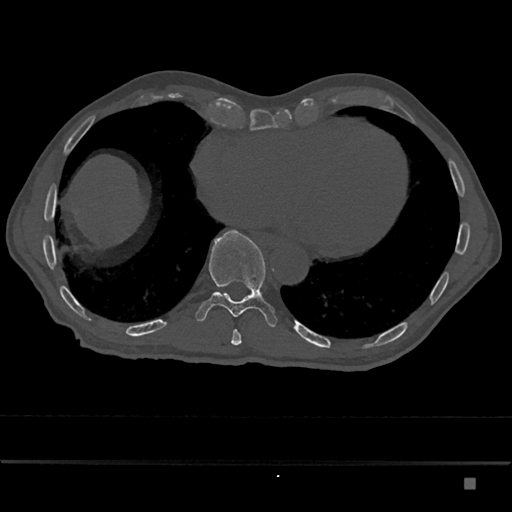
CT including the spine, one axial slice; position 746 of 797 along the scan axis; reconstruction kernel Br40s/3; bone window (W 1800 / L 400 HU); 0.5 mm slice thickness; 512 × 512 image matrix, field of view 390 × 390 mm. Male patient, age 72 years. From the clinical record (not read from this slice): primary cancer: prostate.
Outlined on this slice (semi-automatic segmentation, software-assisted and operator-edited):
- T10 vertebra: box from (x=196, y=230) to (x=277, y=327) px
- T9 vertebra: (x=231, y=330)–(x=242, y=346)